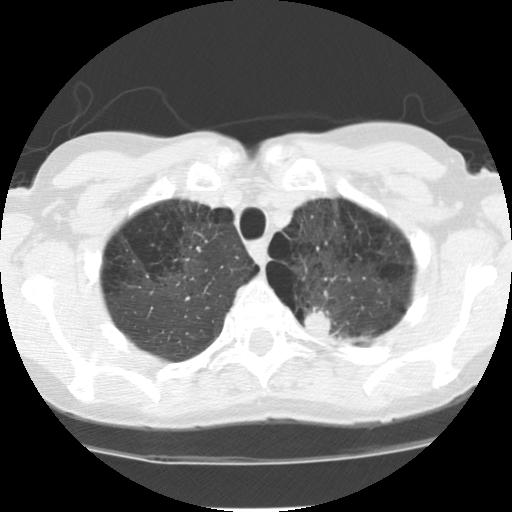
Chest CT (low-dose screening protocol), one axial image, baseline annual screen, lung window (W 1500 / L -600 HU), 2.5 mm slice thickness, standard (soft-tissue) reconstruction kernel (STANDARD), slice 19 of 116 in the series. Female, age 61 years at enrolment.
Lesion marked by an expert reader, bounding box (x1, y1, x2, y2) in pixels: (292, 296, 349, 348). The screening reader recorded 4 non-calcified nodules or masses ≥4 mm on this exam; which of them this box marks is not recorded. Official screen result: positive, change unspecified: nodule(s) >= 4 mm or enlarging nodule(s), mass(es), or other non-specific abnormalities suspicious for lung cancer. Participant outcome: lung cancer diagnosed 68 days after this screen — adenocarcinoma, NOS, left upper lobe, poorly differentiated (G3), stage IB (AJCC 6th edition), 17 mm at pathology.